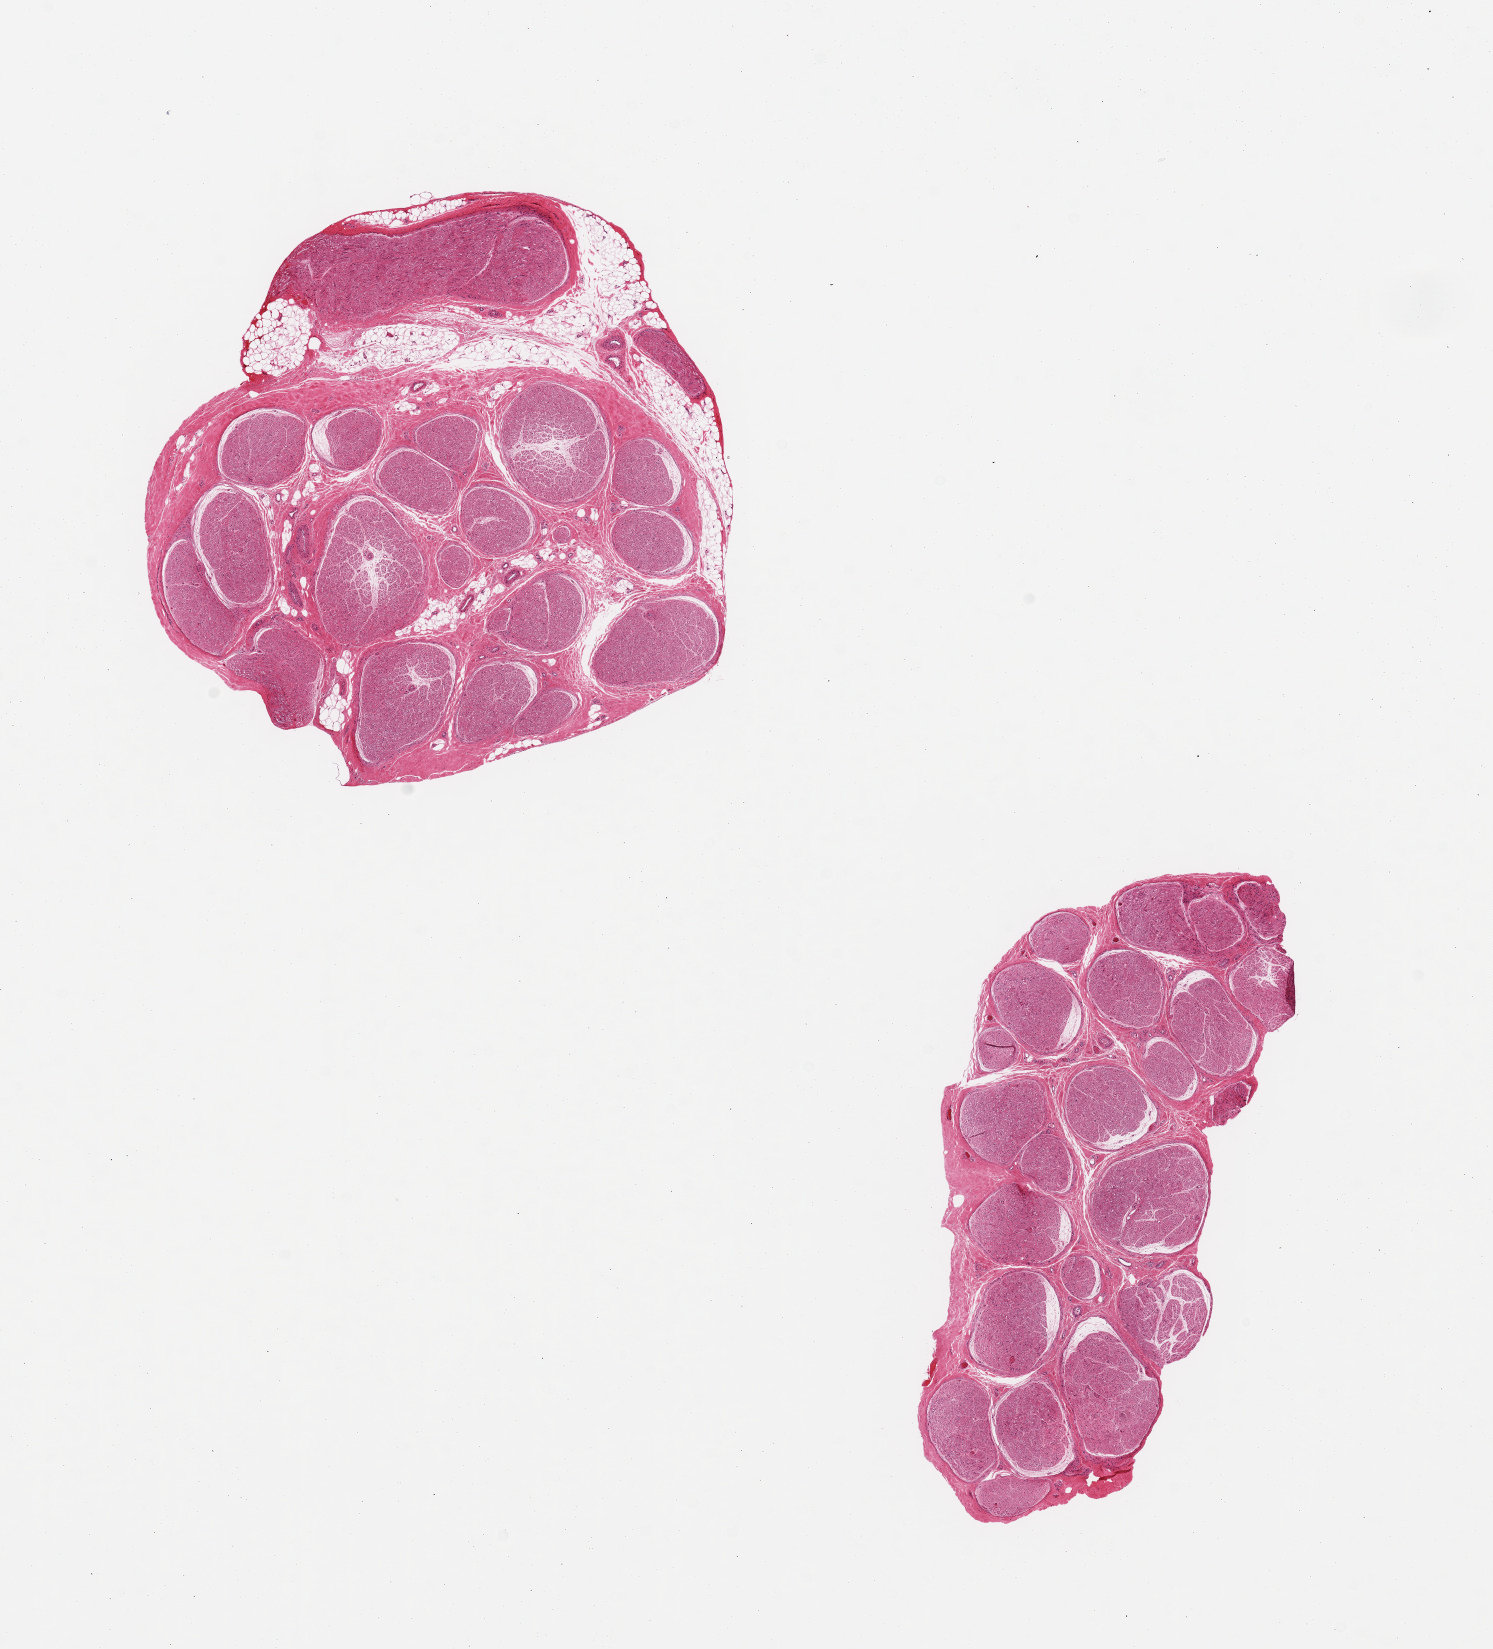
Haematoxylin and eosin whole-slide image — low-resolution overview of the scanned area, about 11.8 x 13.0 mm. PAXgene-fixed, paraffin-embedded tissue. Target tissue: tibial nerve. Tissue donor sample. Male donor.
* review note (as recorded): 2 pieces, trace nubbin of adherent fat, ~0.5mm